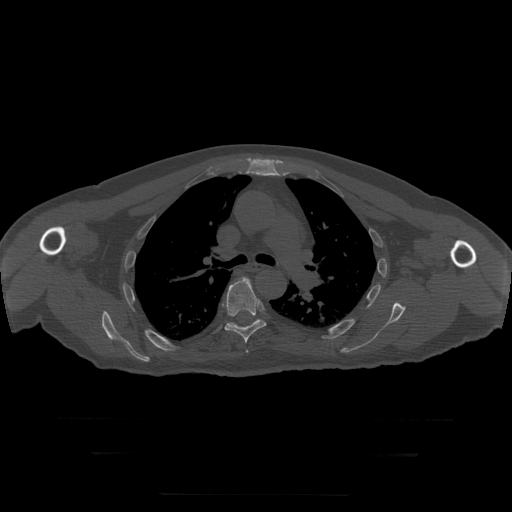
CT including the spine, one axial slice. Reconstruction kernel STANDARD. Bone window (W 1800 / L 400 HU). 1.25 mm slice thickness. 512 × 512 image matrix, field of view 510 × 510 mm. Patient age 73 years. Case-level facts recorded for this patient, not image findings: primary cancer: prostate.
Annotated regions visible in this slice (semi-automatic segmentation, software-assisted and operator-edited):
- T5 vertebra: bounding box [x1, y1, x2, y2] px = [246, 350, 249, 353]
- T6 vertebra: [225, 278, 266, 344]
- T7 vertebra: [230, 320, 258, 325]